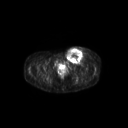
FDG PET of an extremity soft-tissue mass (from a PET/CT study), one axial slice. Position 63 of 267 along the scan axis. 3.27 mm slice thickness. 128 × 128 image matrix, field of view 600 × 600 mm. Female patient, age 24 years. Case-level facts recorded for this patient, not image findings: histological type: leiomyosarcoma; grade: high; site of the primary tumour: groin.
Outlined on this slice (expert contour drawn on MRI and transferred to this co-registered scan by the dataset authors):
- gross tumour volume including surrounding oedema: bounding box [x1, y1, x2, y2] px = [65, 46, 91, 64]
- gross tumour volume (mass): [65, 48, 83, 64]